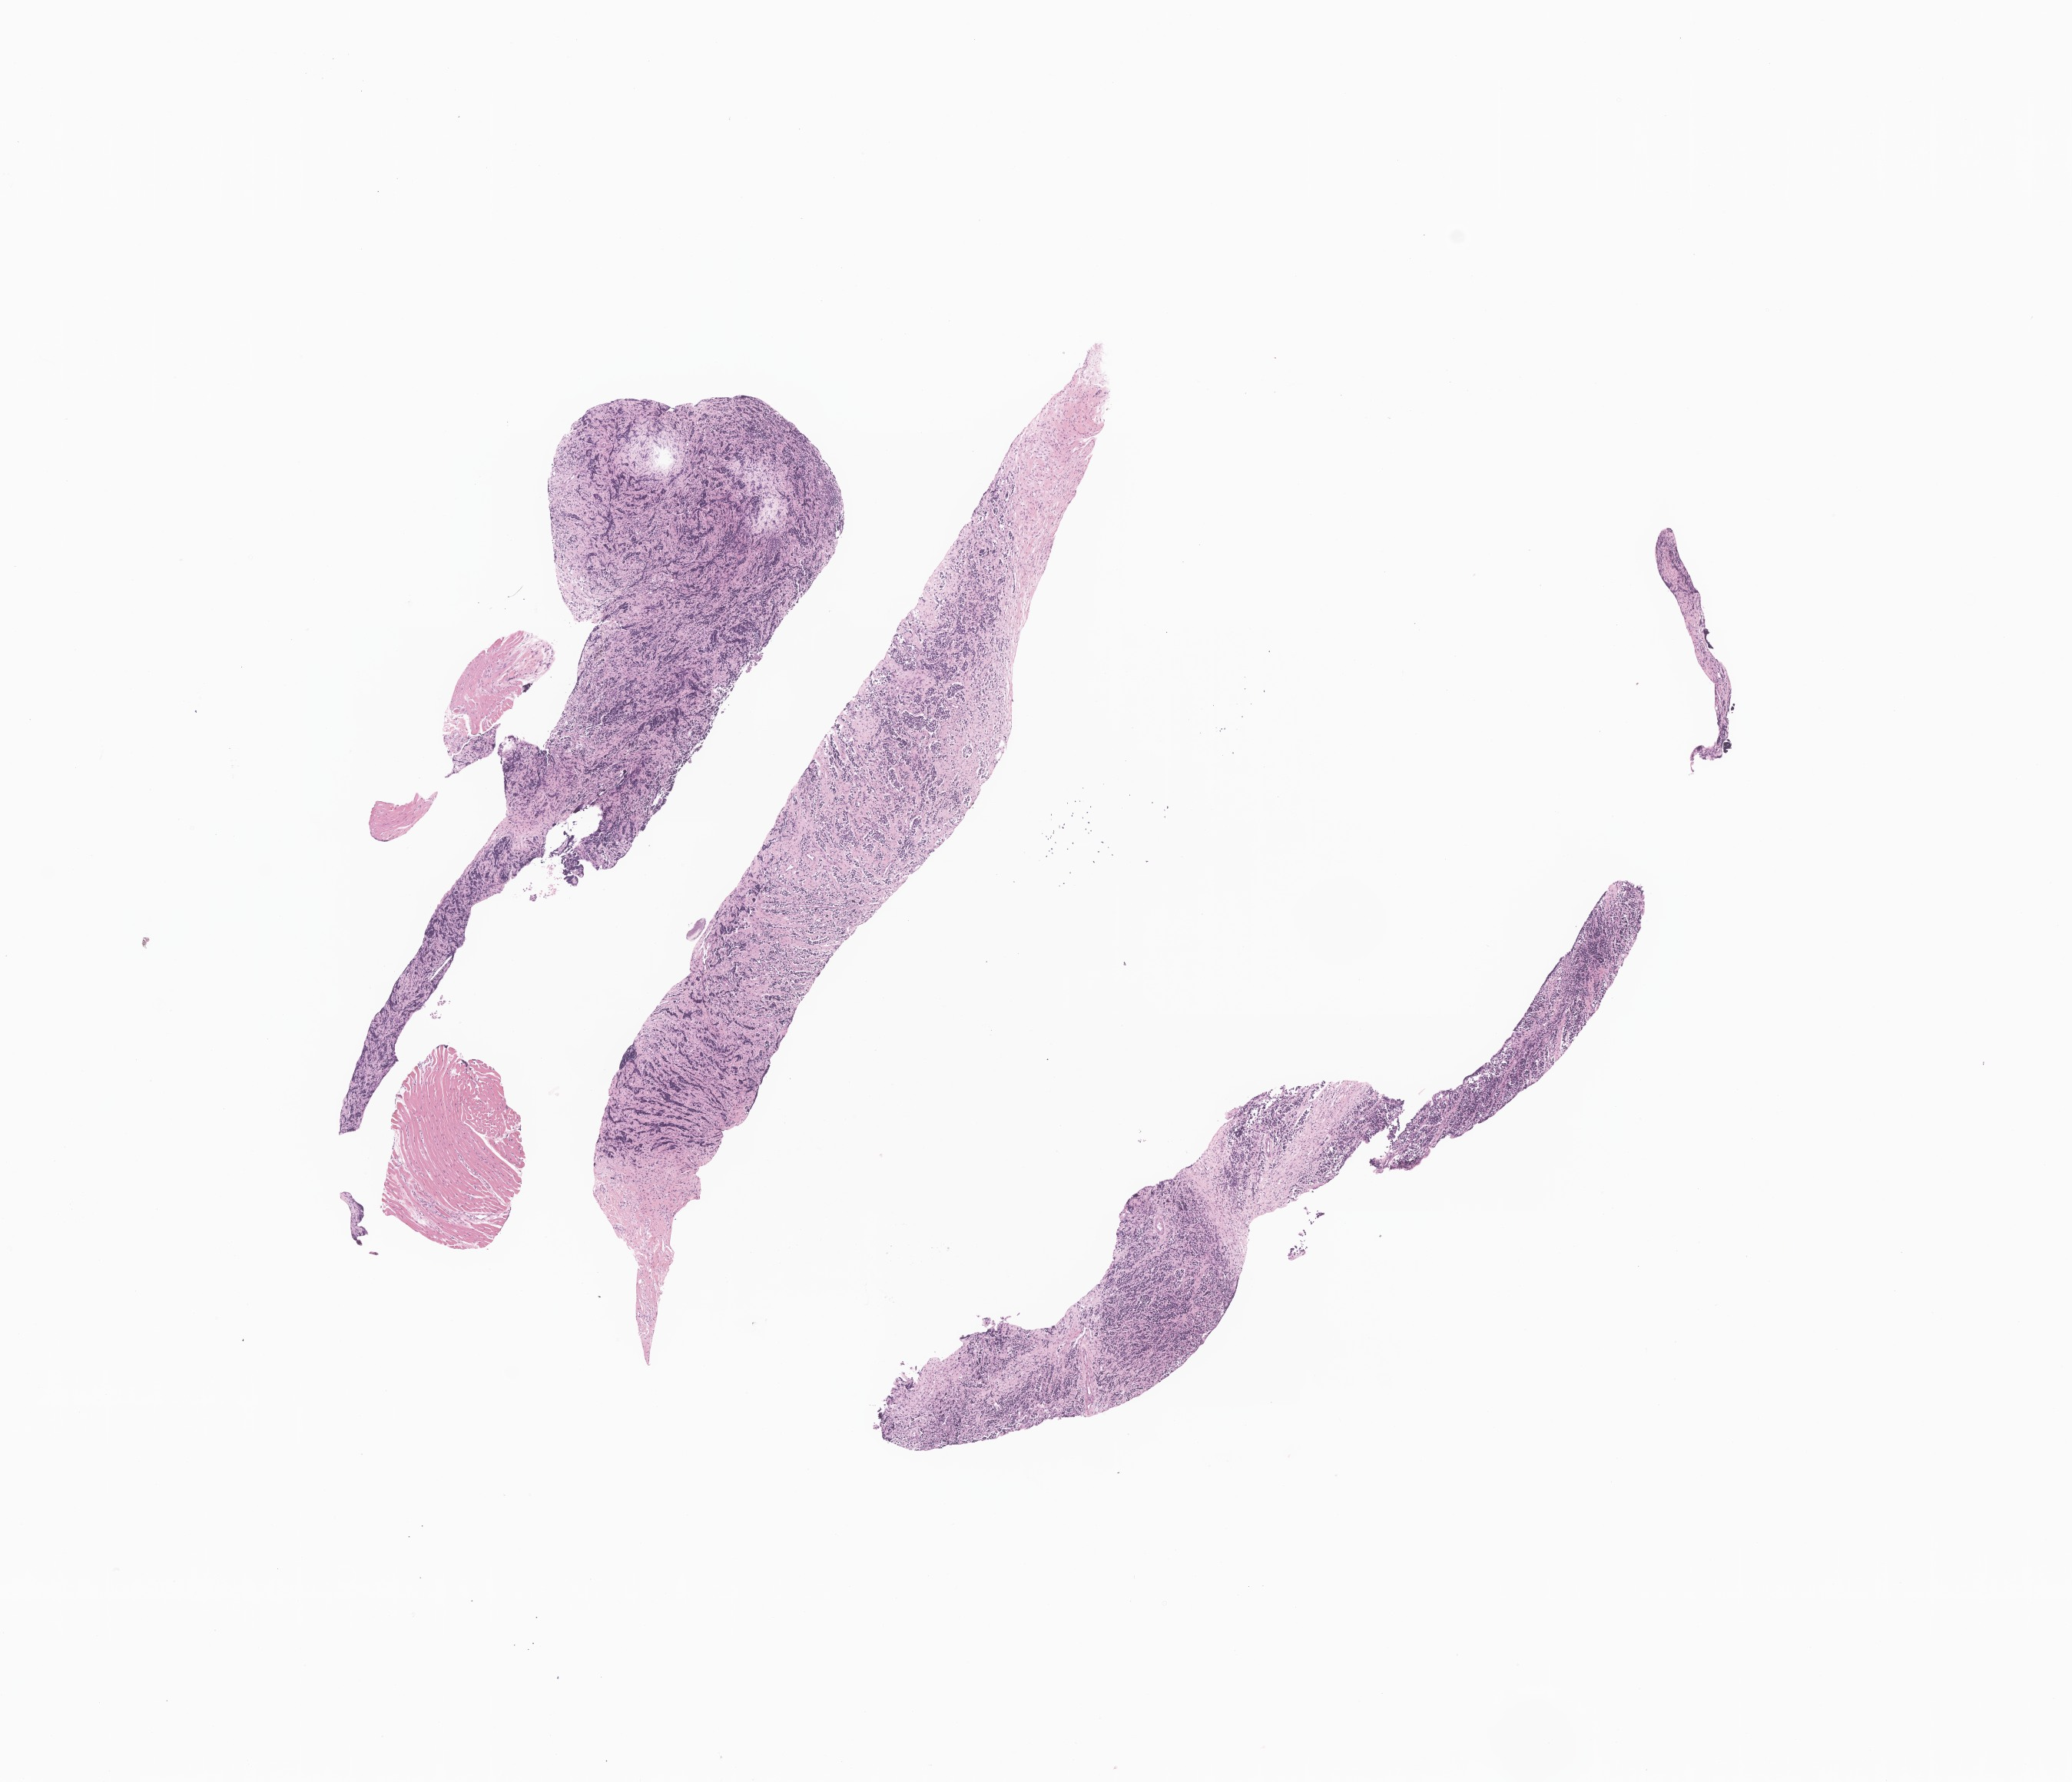
Digitized haematoxylin and eosin-stained section of tumor tissue from the adrenal gland, a low-resolution overview of the entire scanned area, about 11.4 x 9.8 mm, formalin-fixed paraffin-embedded section. Patient: male, age 167 days.
• recorded diagnosis: Neuroblastoma, NOS